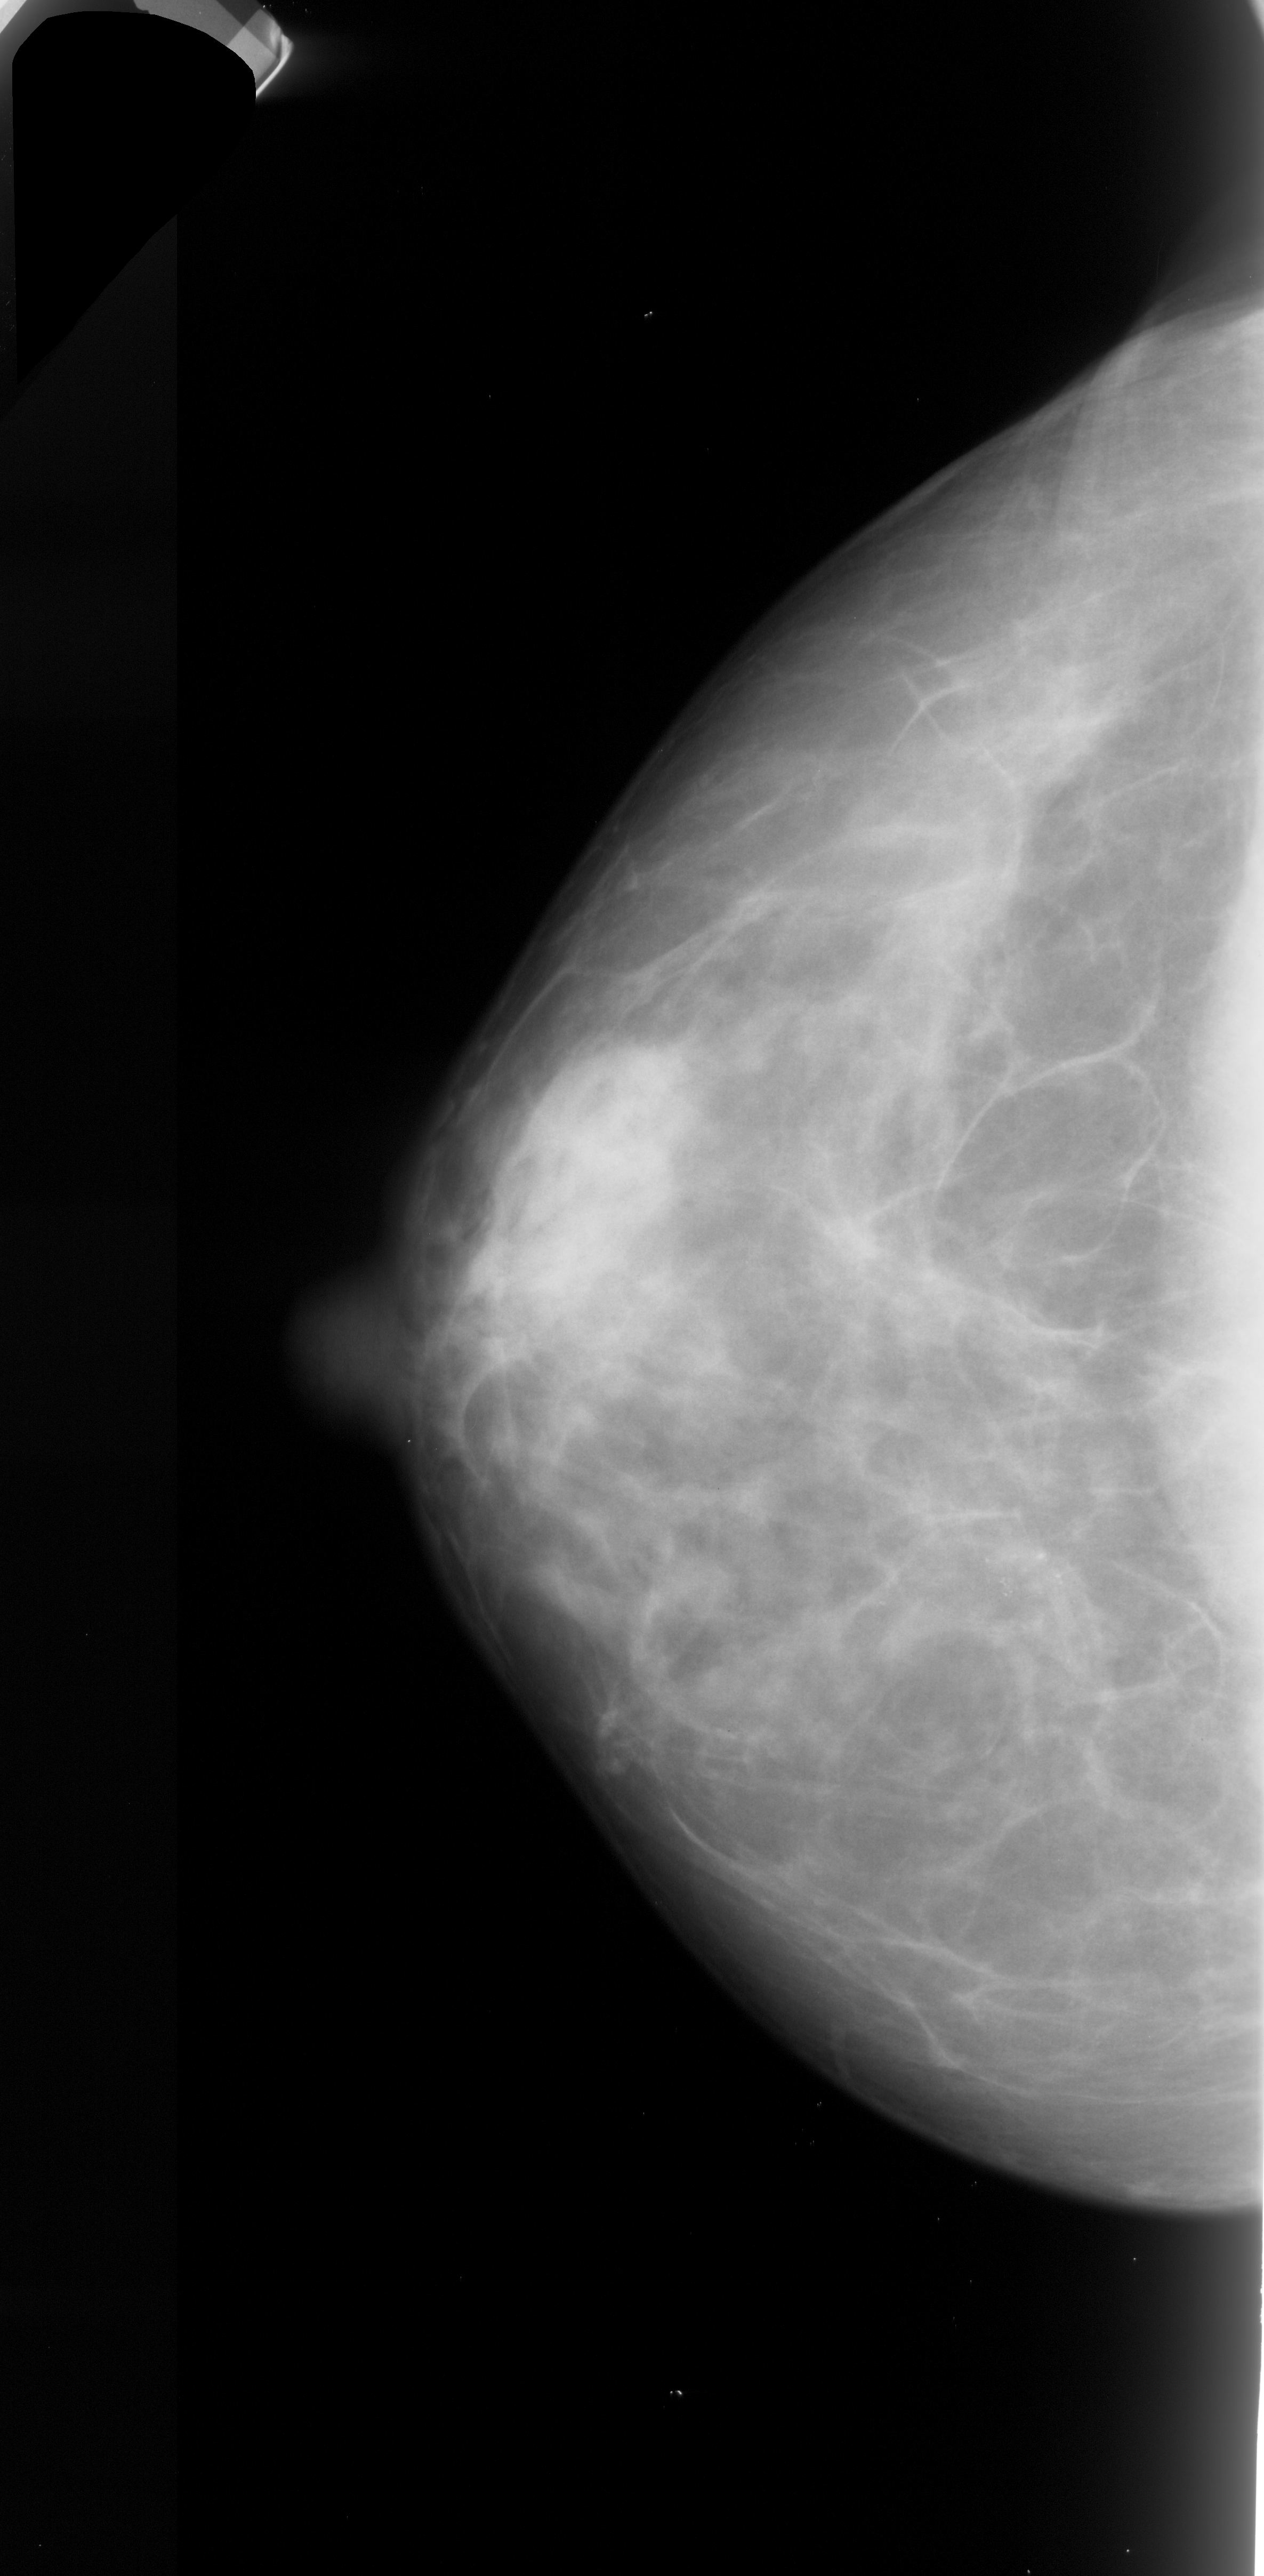
Digitized screen-film mammogram; left breast; CC view; BI-RADS breast density category 1 (scale 1–4); 1264 × 2576 image matrix.
Marked abnormalities (boxes around the expert regions of interest):
- calcifications, morphology pleomorphic, distribution clustered; BI-RADS assessment category 4; subtlety rating 3 on a 1 (subtle) to 5 (obvious) scale; pathology result (as recorded, not read from the image): malignant: box from (x=968, y=1510) to (x=1103, y=1679) px